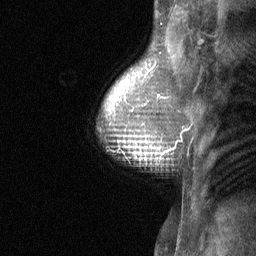
Breast MRI (dynamic contrast-enhanced), one sagittal slice; slice 49 of 64 in the series (ordered by position); dynamic contrast-enhanced study with each time point stored as its own series, time point 2 of 3 at this slice position (early post-contrast, ordered by acquisition time); 1.5 T; TE 4.8 ms, TR 27 ms; 2 mm slice thickness; 256 × 256 image matrix, field of view 180 × 180 mm. Female patient, age 47 years. Case-level facts recorded for this patient, not image findings: setting: breast cancer imaged before/during neoadjuvant chemotherapy; receptor status: HR-positive, HER2-negative.
Outlined on this slice (semi-automatic segmentation, software-assisted and operator-edited):
- analysis volume of interest (the breast-tissue region the enhancement analysis was run in; not a lesion): bounding box [x1, y1, x2, y2] px = [104, 138, 165, 170]
- tumour enhancement mask (voxels above the 90 % enhancement threshold inside the analysis volume of interest): [143, 153, 163, 160]